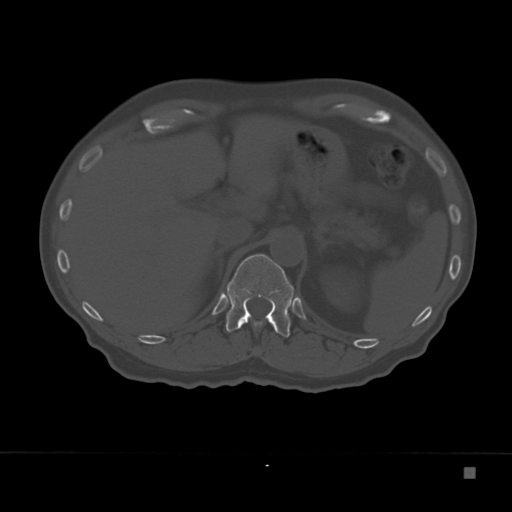
CT including the spine, one axial slice. Slice 136 of 332 in the series (ordered by position). Reconstruction kernel Br40s. 120 kVp. Bone window (W 1800 / L 400 HU). 1.5 mm slice thickness. 512 × 512 image matrix, field of view 389 × 389 mm. Male patient, age 72 years. From the clinical record (not read from this slice): primary cancer: skeletal.
Annotated regions visible in this slice (semi-automatic segmentation, software-assisted and operator-edited):
- T12 vertebra: bounding box <225,254,294,337> (left, top, right, bottom; pixels)